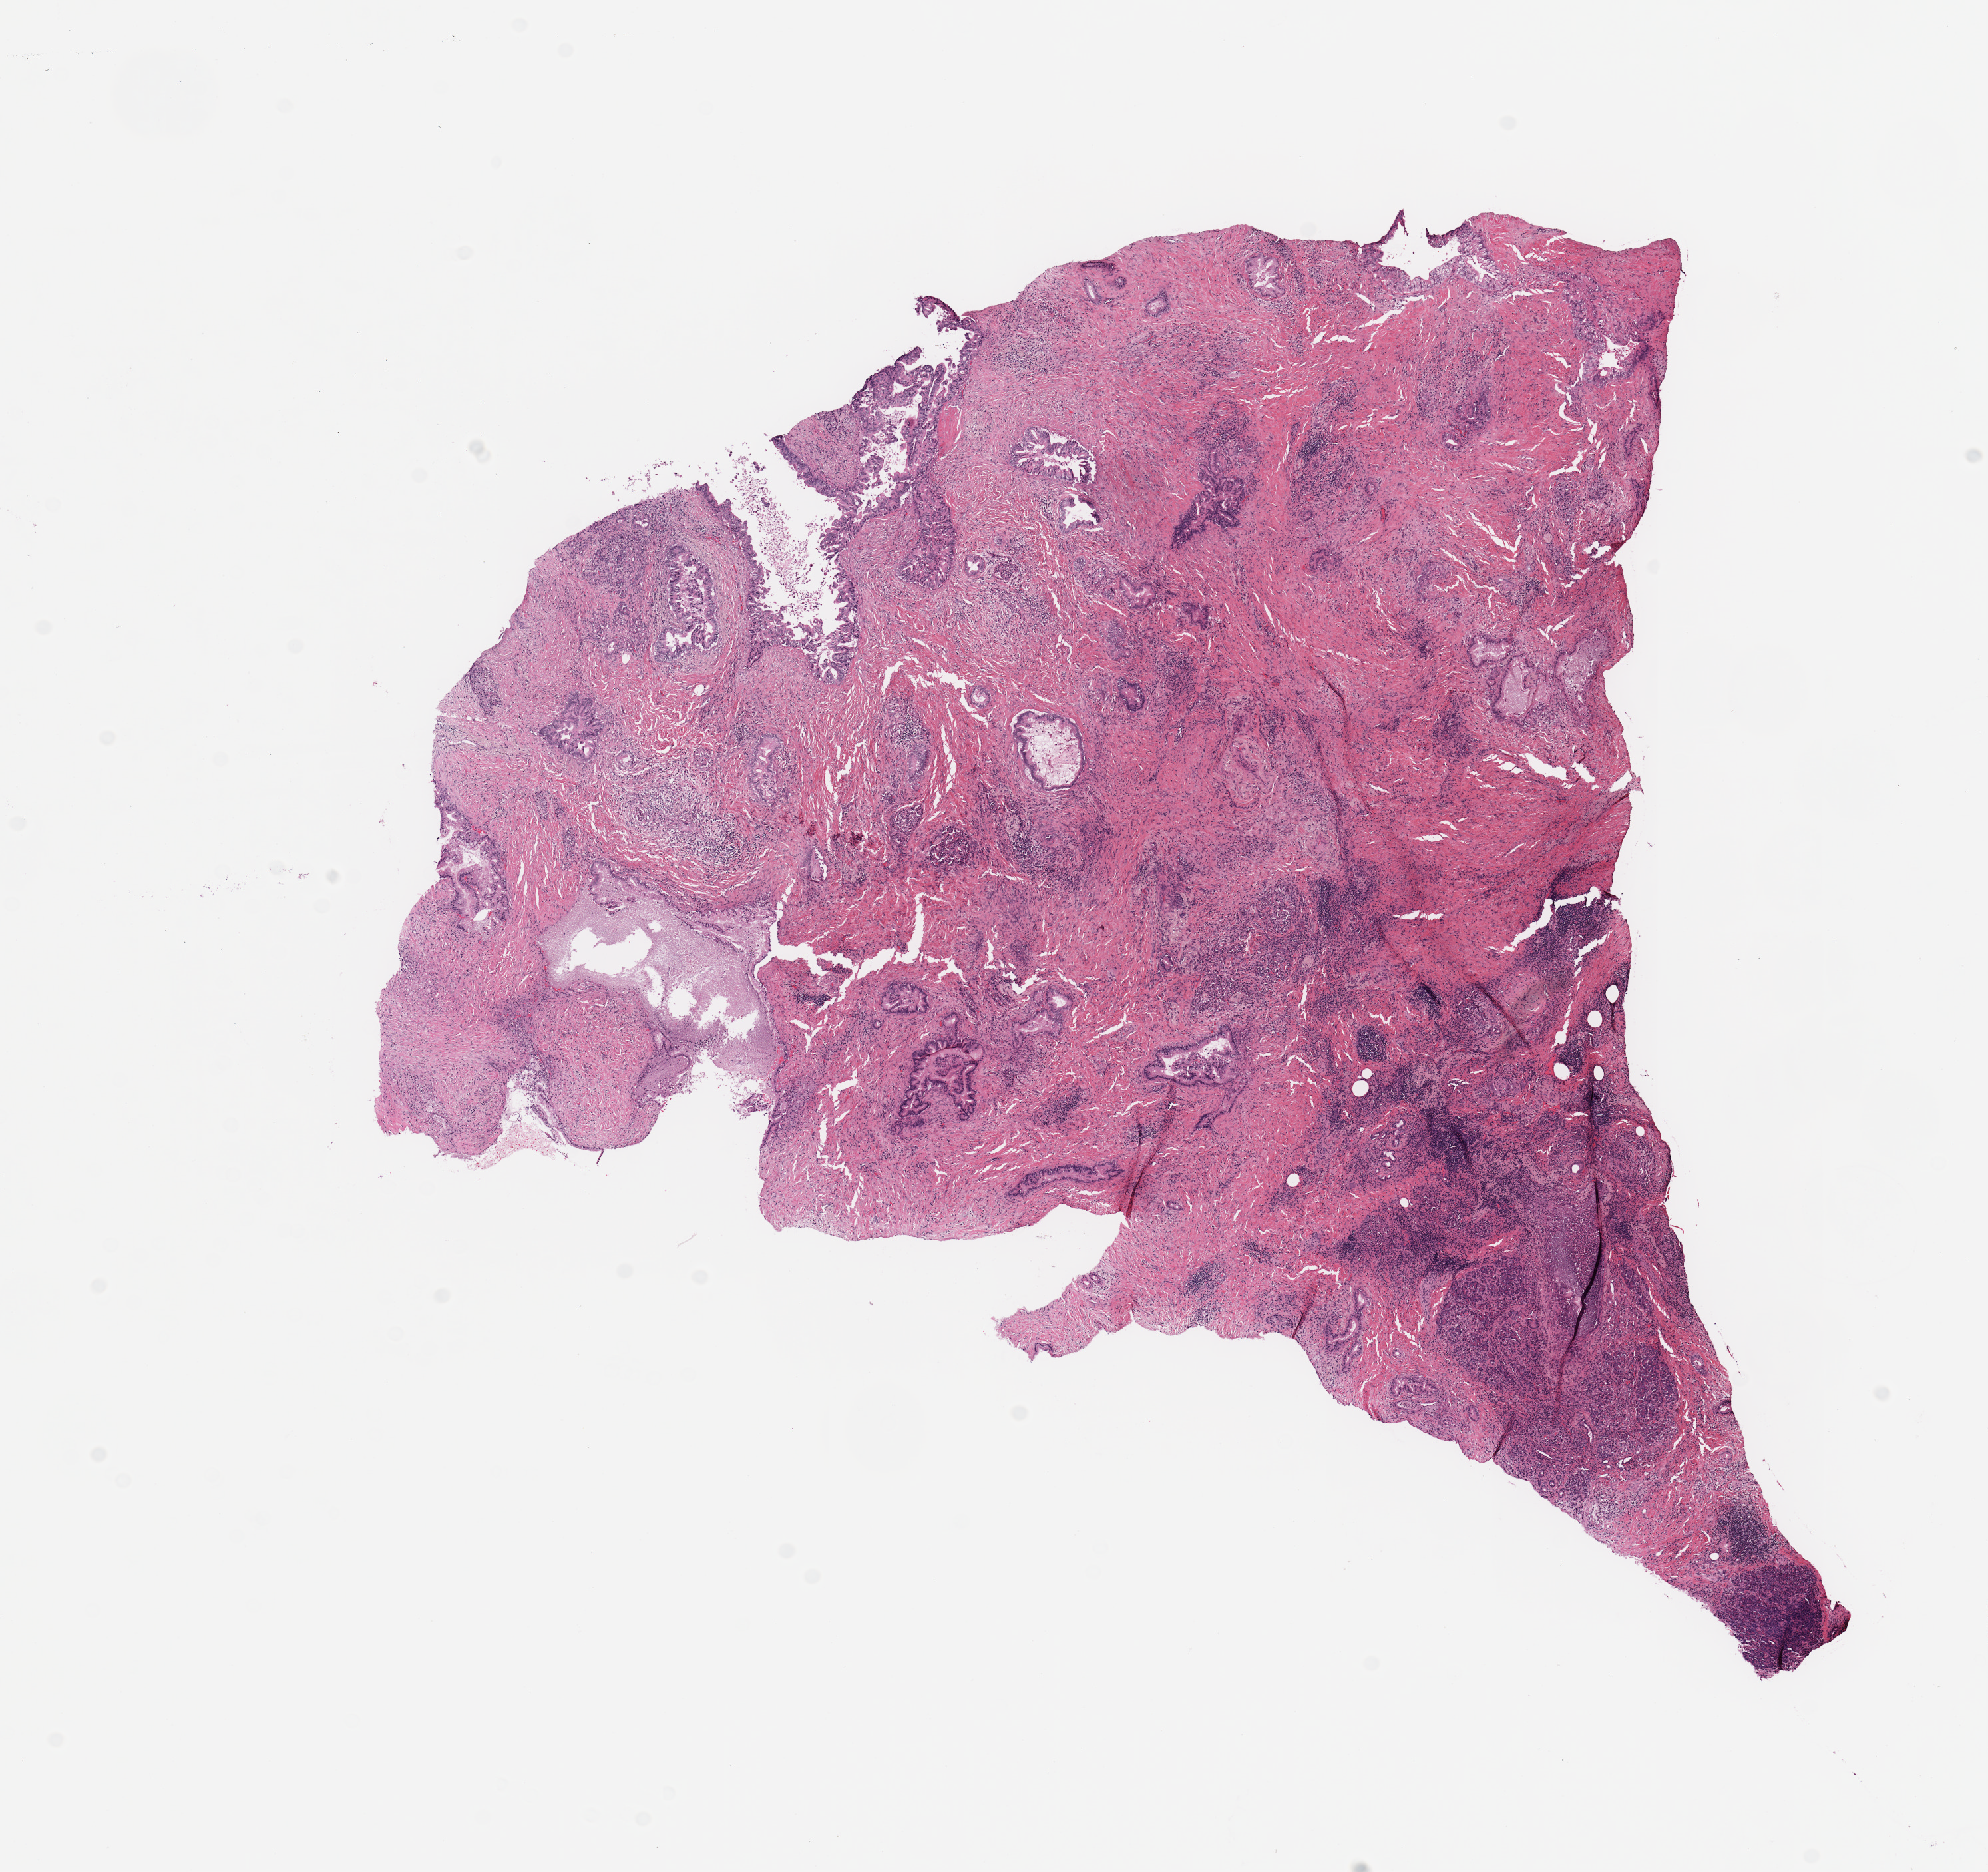
Whole-slide histology image, H&E — whole scanned area (about 11.8 x 11.1 mm) shown as a low-resolution overview. Tumour tissue sample, sampled site: pancreas. Female, 65 y/o. Composition of this section per pathologist review: tumour nuclei 10%, necrosis 0%.
Histologic diagnosis: Infiltrating duct carcinoma, NOS.